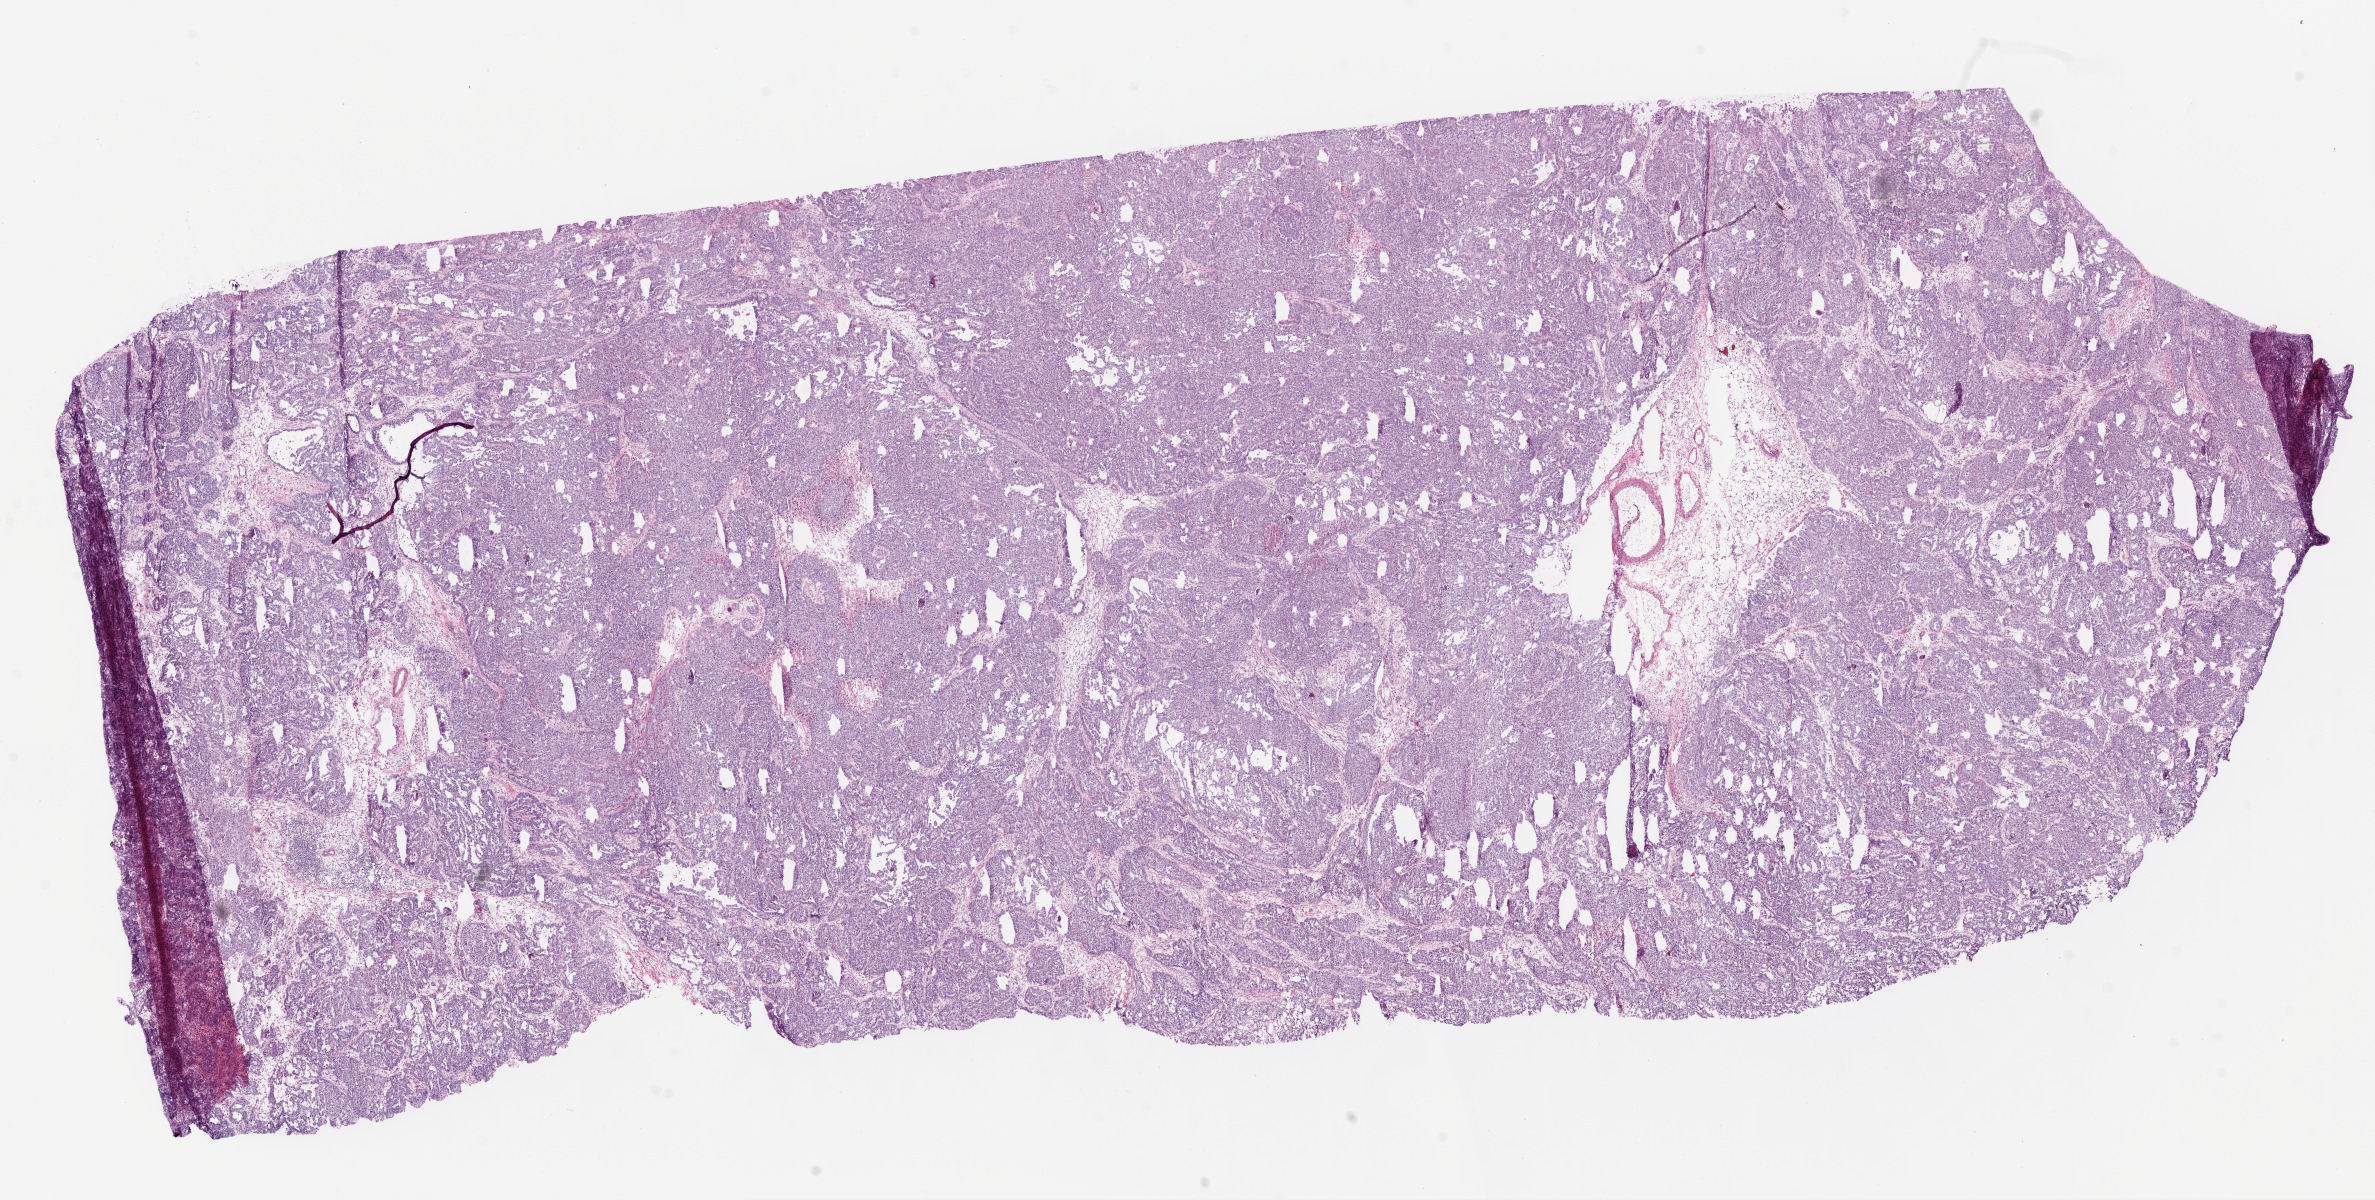
Whole-slide histology image, H&E, low-resolution overview of the scanned area, about 19.1 x 9.6 mm (slide scanned at 20x). Frozen section from the bottom of the tissue portion. Primary tumour sample from the ovary. Female patient; age at initial diagnosis 58 years. Histologic grade: G3 (poorly differentiated). Slide review estimates, as recorded: tumour cells 87%, tumour nuclei 90%, normal cells 0%, stromal cells 8%, necrosis 5%.
Pathologic diagnosis: Serous cystadenocarcinoma, NOS. Laterality: bilateral. FIGO stage: IIIC.